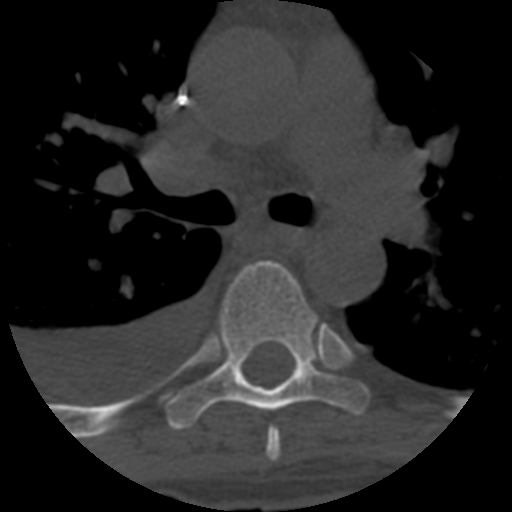
CT including the spine, one axial slice. Slice 438 of 708 in the series (ordered by position). Reconstruction kernel STANDARD. 120 kVp. One of 3 acquisitions stored at this slice position. Bone window (W 1800 / L 400 HU). 1.25 mm slice thickness. 512 × 512 image matrix. Patient age 55 years. Case-level facts recorded for this patient, not image findings: primary cancer: colon; vertebrae with lytic lesions (as recorded): T12, L1, L5.
Structures marked on this image (semi-automatic segmentation, software-assisted and operator-edited):
- T5 vertebra: box from (x=266, y=428) to (x=281, y=461) px
- T6 vertebra: (x=166, y=260)–(x=370, y=429)